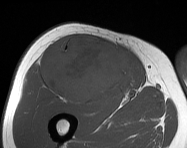
MRI of an extremity soft-tissue mass, one axial slice. Slice 86 of 114 in the series (ordered by position). MR volume resampled by the dataset authors to the PET/CT grid (not the native acquisition matrix). 3.27 mm slice thickness. 187 × 148 image matrix. Male patient. Case-level facts recorded for this patient, not image findings: histological type: pleiomorphic leiomyosarcoma; grade: intermediate; site of the primary tumour: right thigh.
Annotated regions visible in this slice (expert contour drawn on MRI and transferred to this co-registered scan by the dataset authors):
- gross tumour volume including surrounding oedema: bounding box (x1, y1, x2, y2) in pixels: (43, 36, 133, 103)
- gross tumour volume (mass): (43, 36, 133, 103)